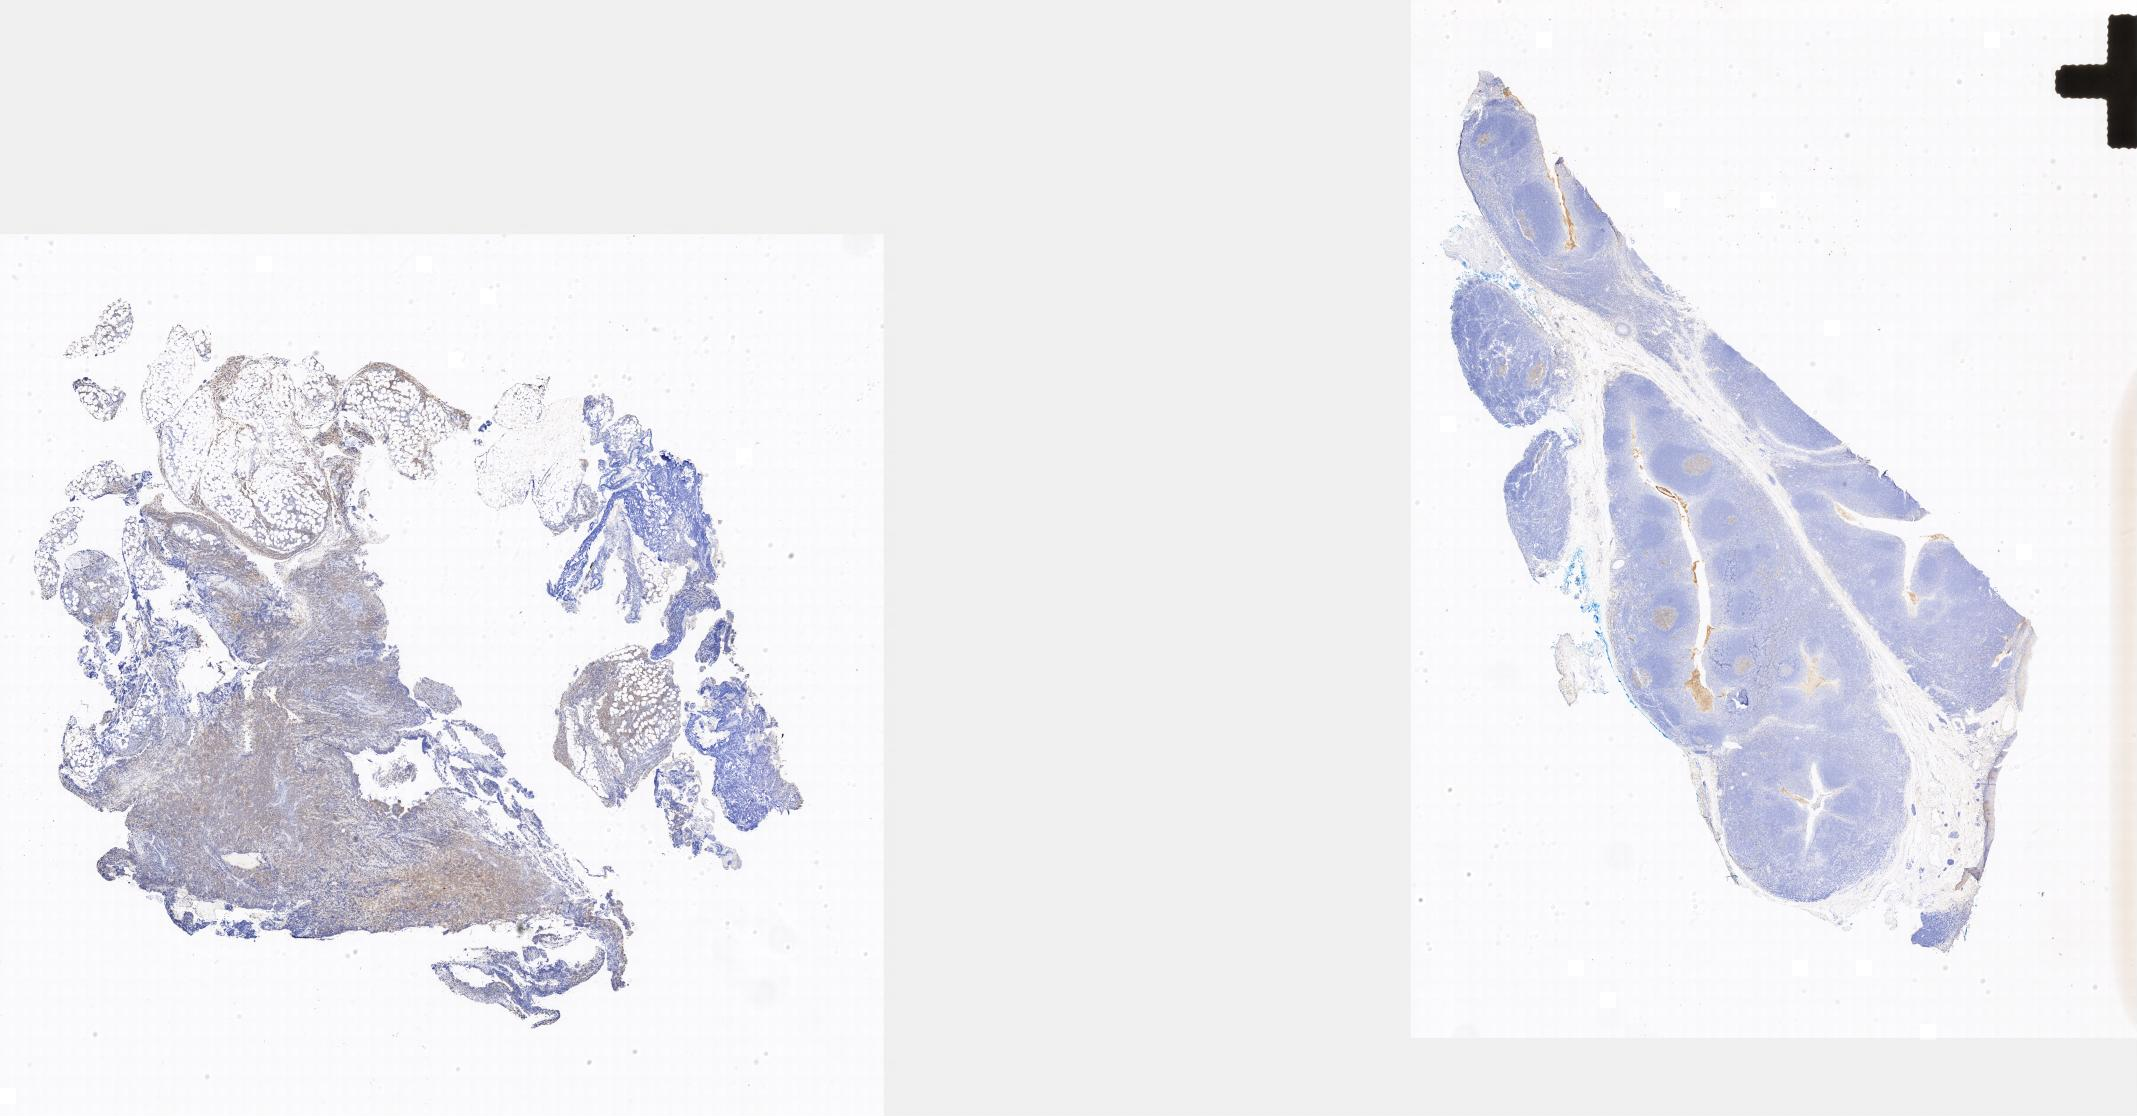
IHC for CD10, whole-slide image, low-resolution overview of the scanned area. Tumor tissue. Anatomic site: abdominal lymph node. Patient: male, age at initial diagnosis 9 years.
Diagnosis: Burkitt lymphoma, NOS.